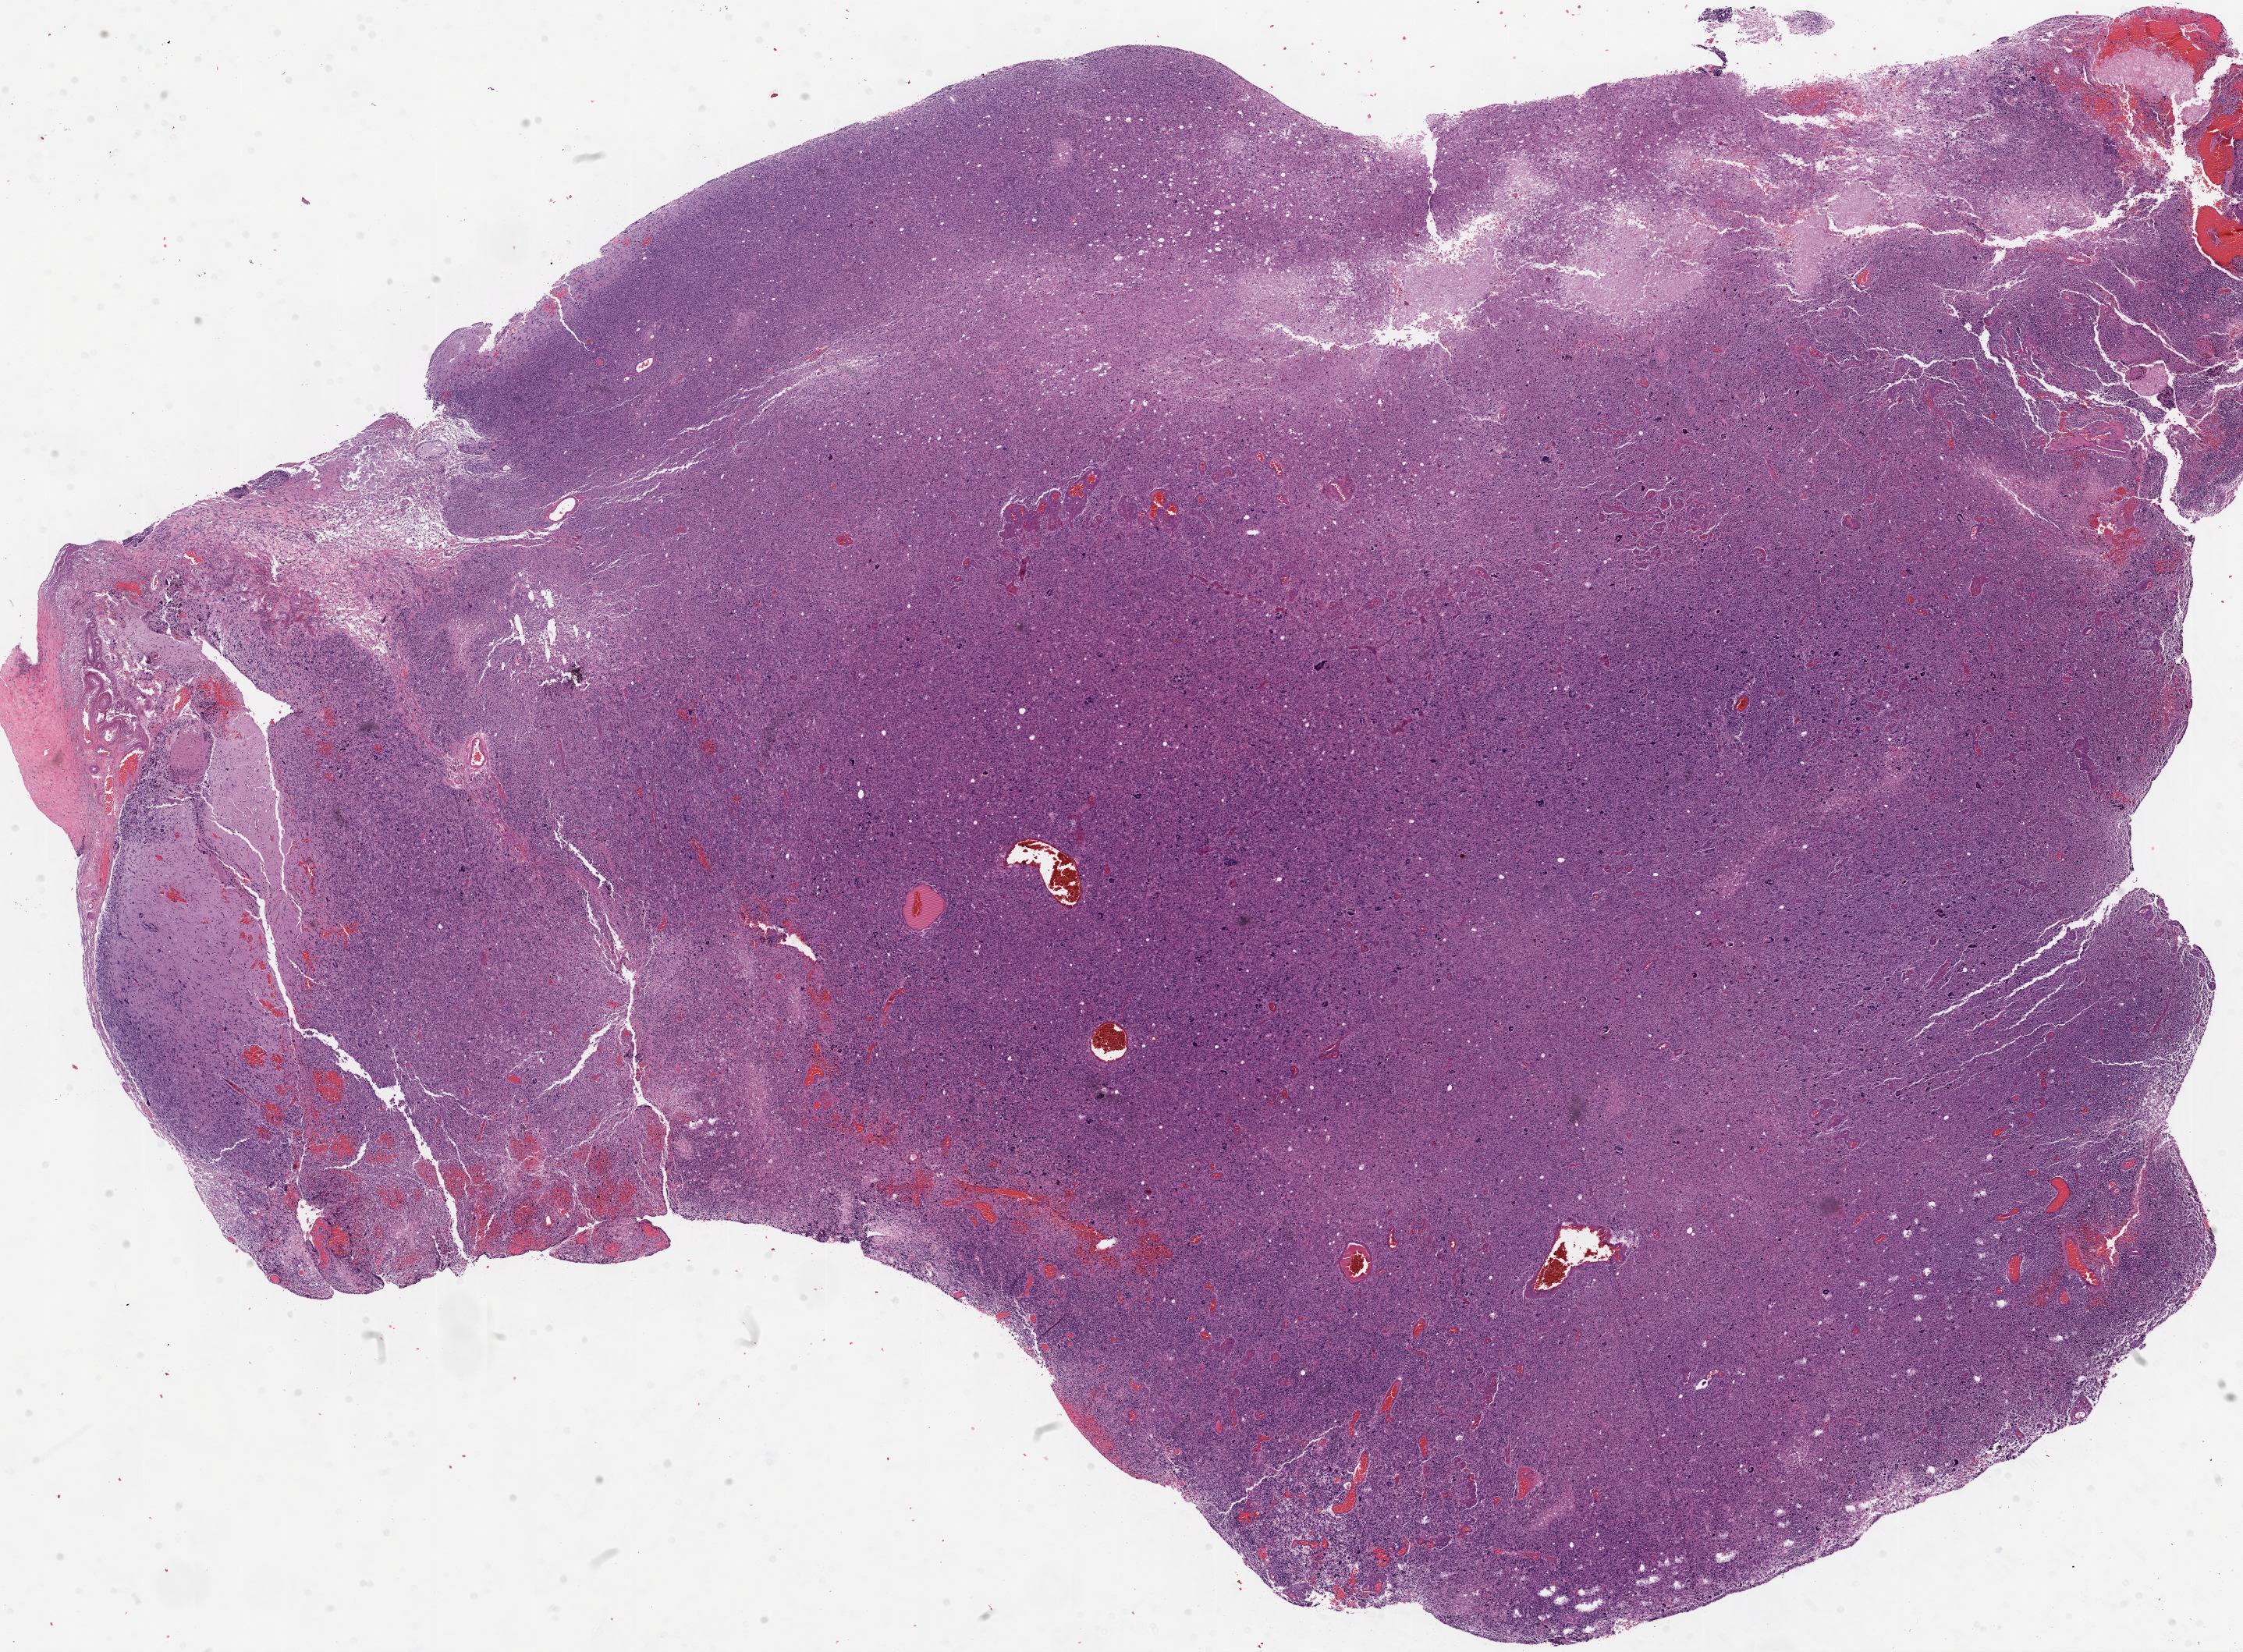
Digitized H&E tissue section (whole slide), a low-resolution overview of the entire scanned area, about 23.1 x 17.0 mm (from a 20x scan); formalin-fixed paraffin-embedded (FFPE) diagnostic section; brain, primary tumour sample. Patient: male, age at initial diagnosis 27 years.
- pathologic diagnosis: Glioblastoma